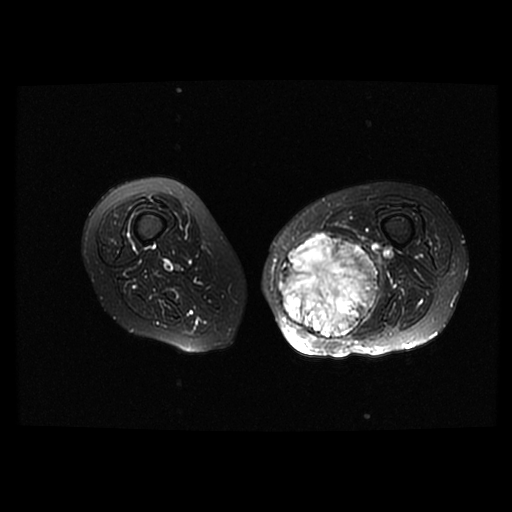
MRI of an extremity soft-tissue mass, one axial slice; position 28 of 42 along the scan axis; T2-weighted fat-saturated; 6 mm slice thickness; 512 × 512 image matrix, field of view 420 × 420 mm. Female patient. From the clinical record (not read from this slice): histological type: pleomorphic leiomyosarcoma; grade: high; site of the primary tumour: left thigh.
Outlined on this slice (expert manual segmentation):
- gross tumour volume including surrounding oedema: bounding box (x1, y1, x2, y2) in pixels: (277, 233, 384, 340)
- gross tumour volume (mass): (277, 233, 379, 338)